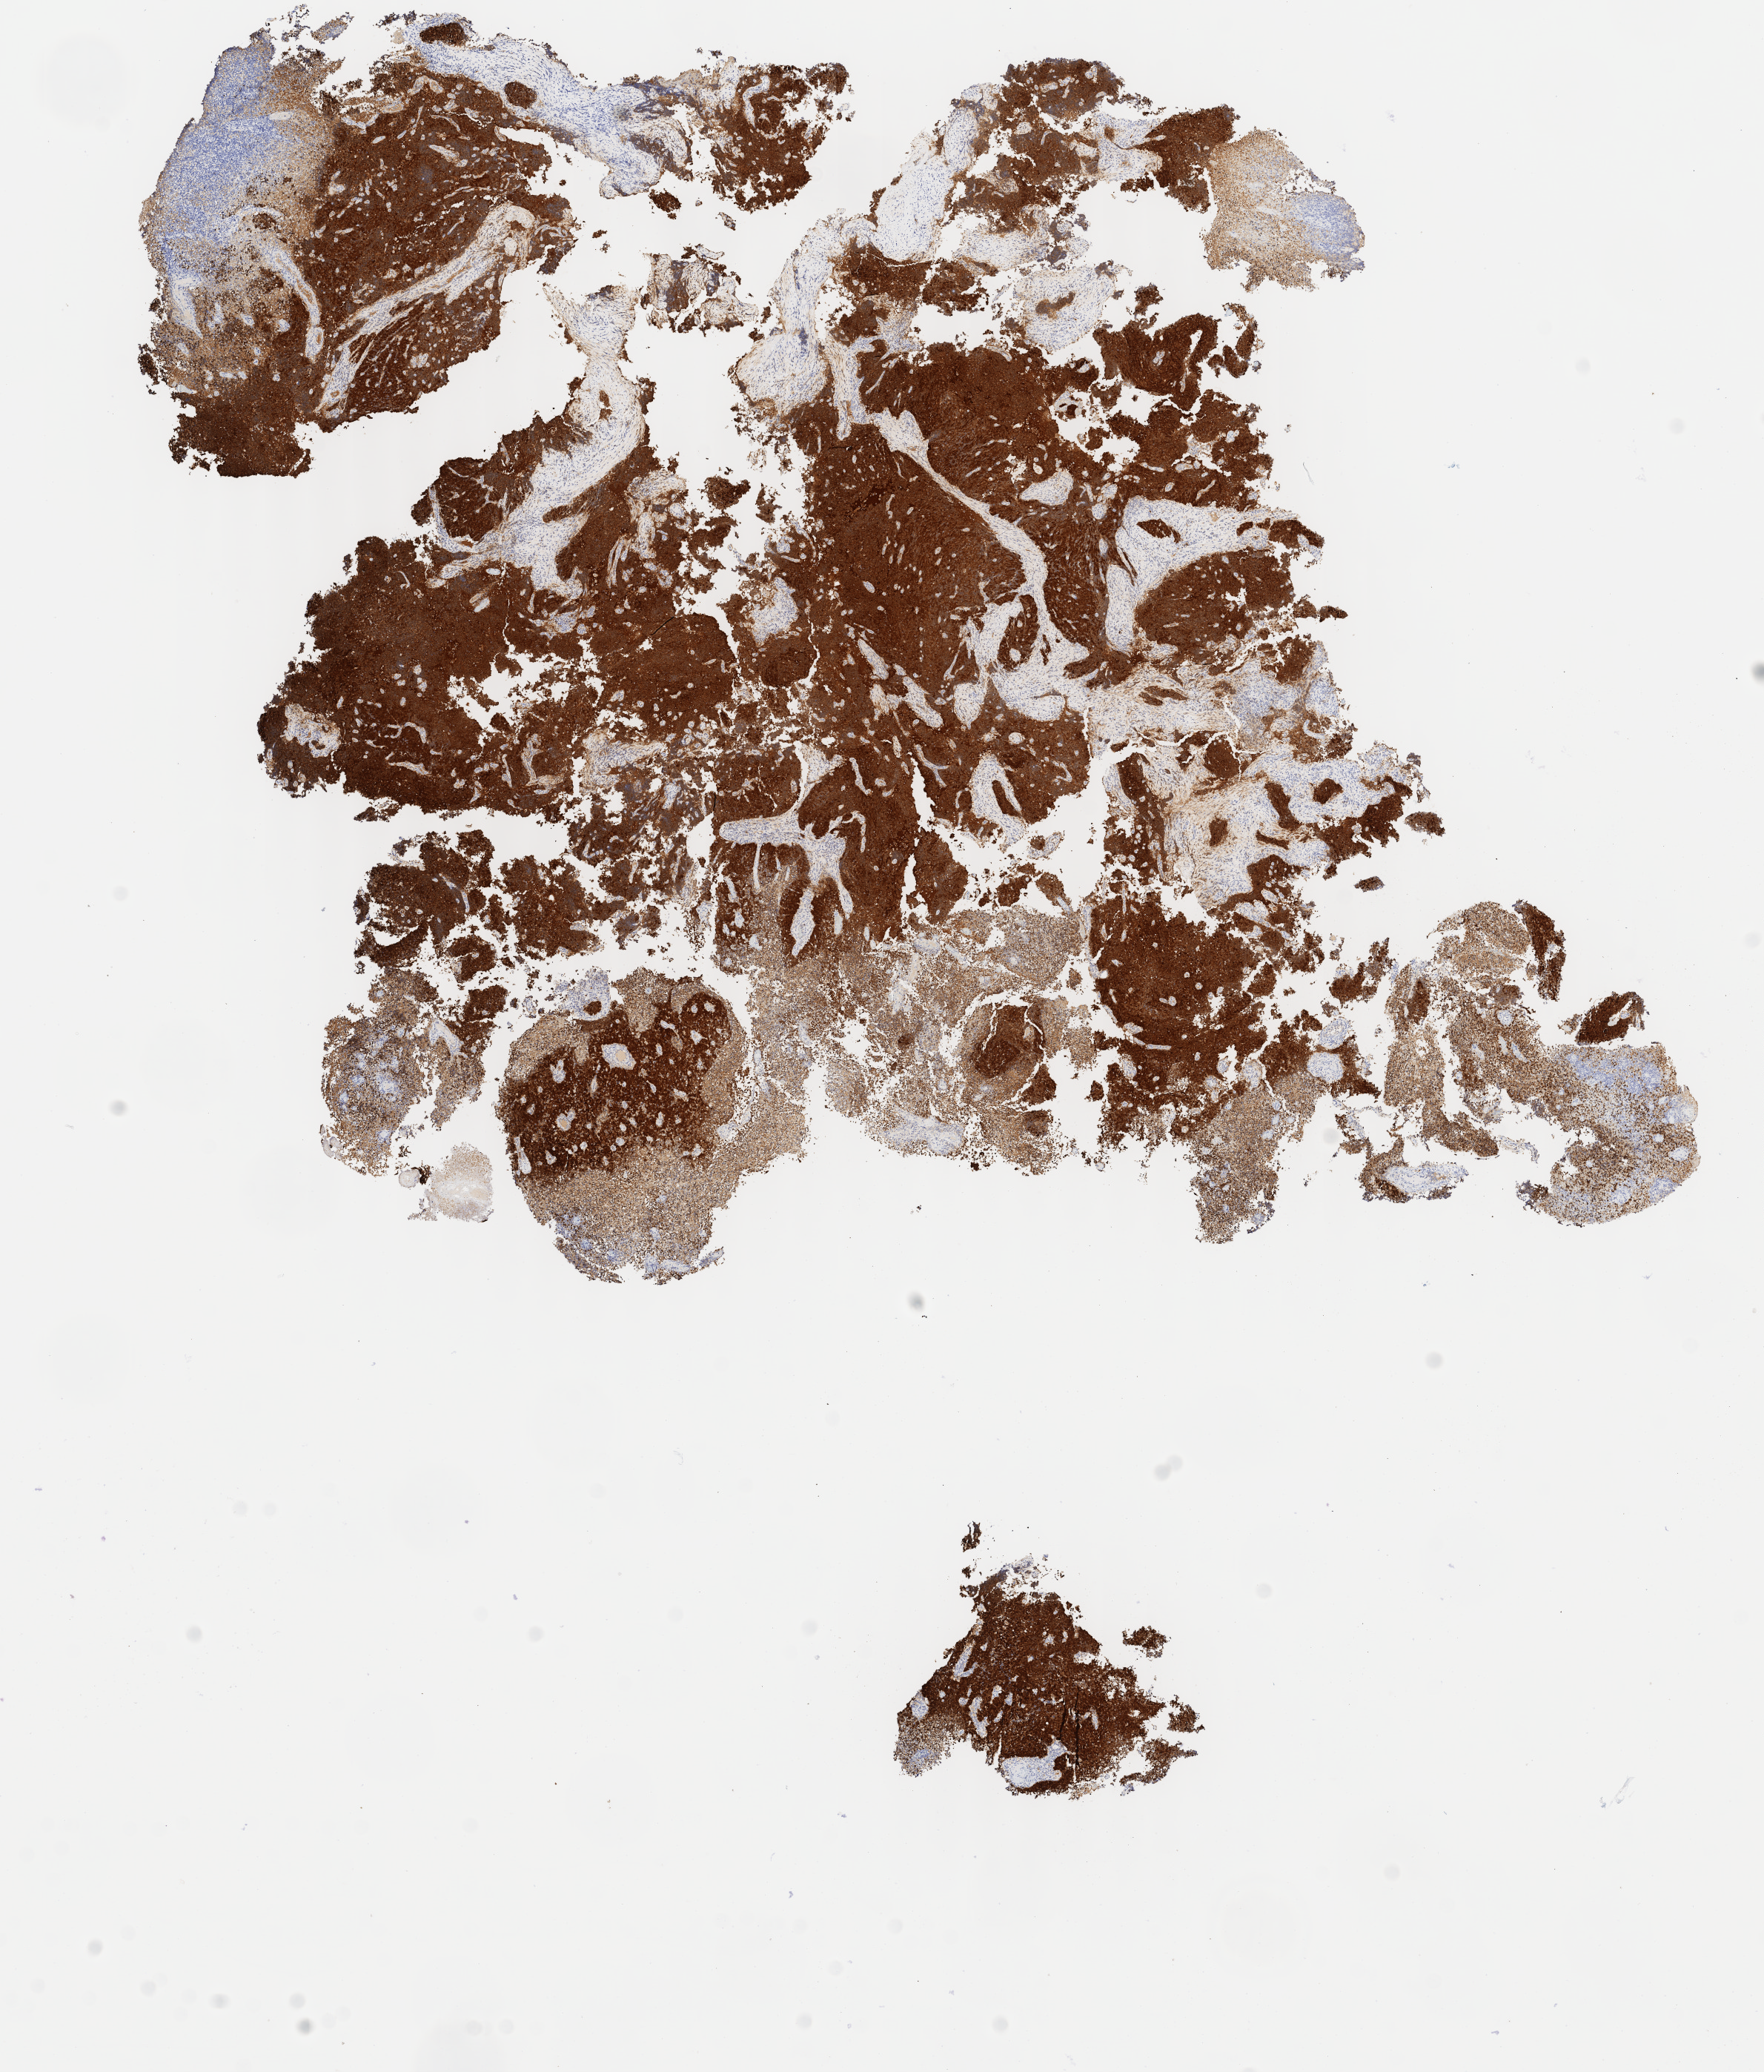
Whole-slide image, immunohistochemical stain for p16 (p16INK4a), low-resolution overview of the scanned area, about 9.5 x 11.1 mm; tumor tissue; site: cervix. Patient: female, age 41 years.
Histologic diagnosis: Small cell carcinoma, NOS.